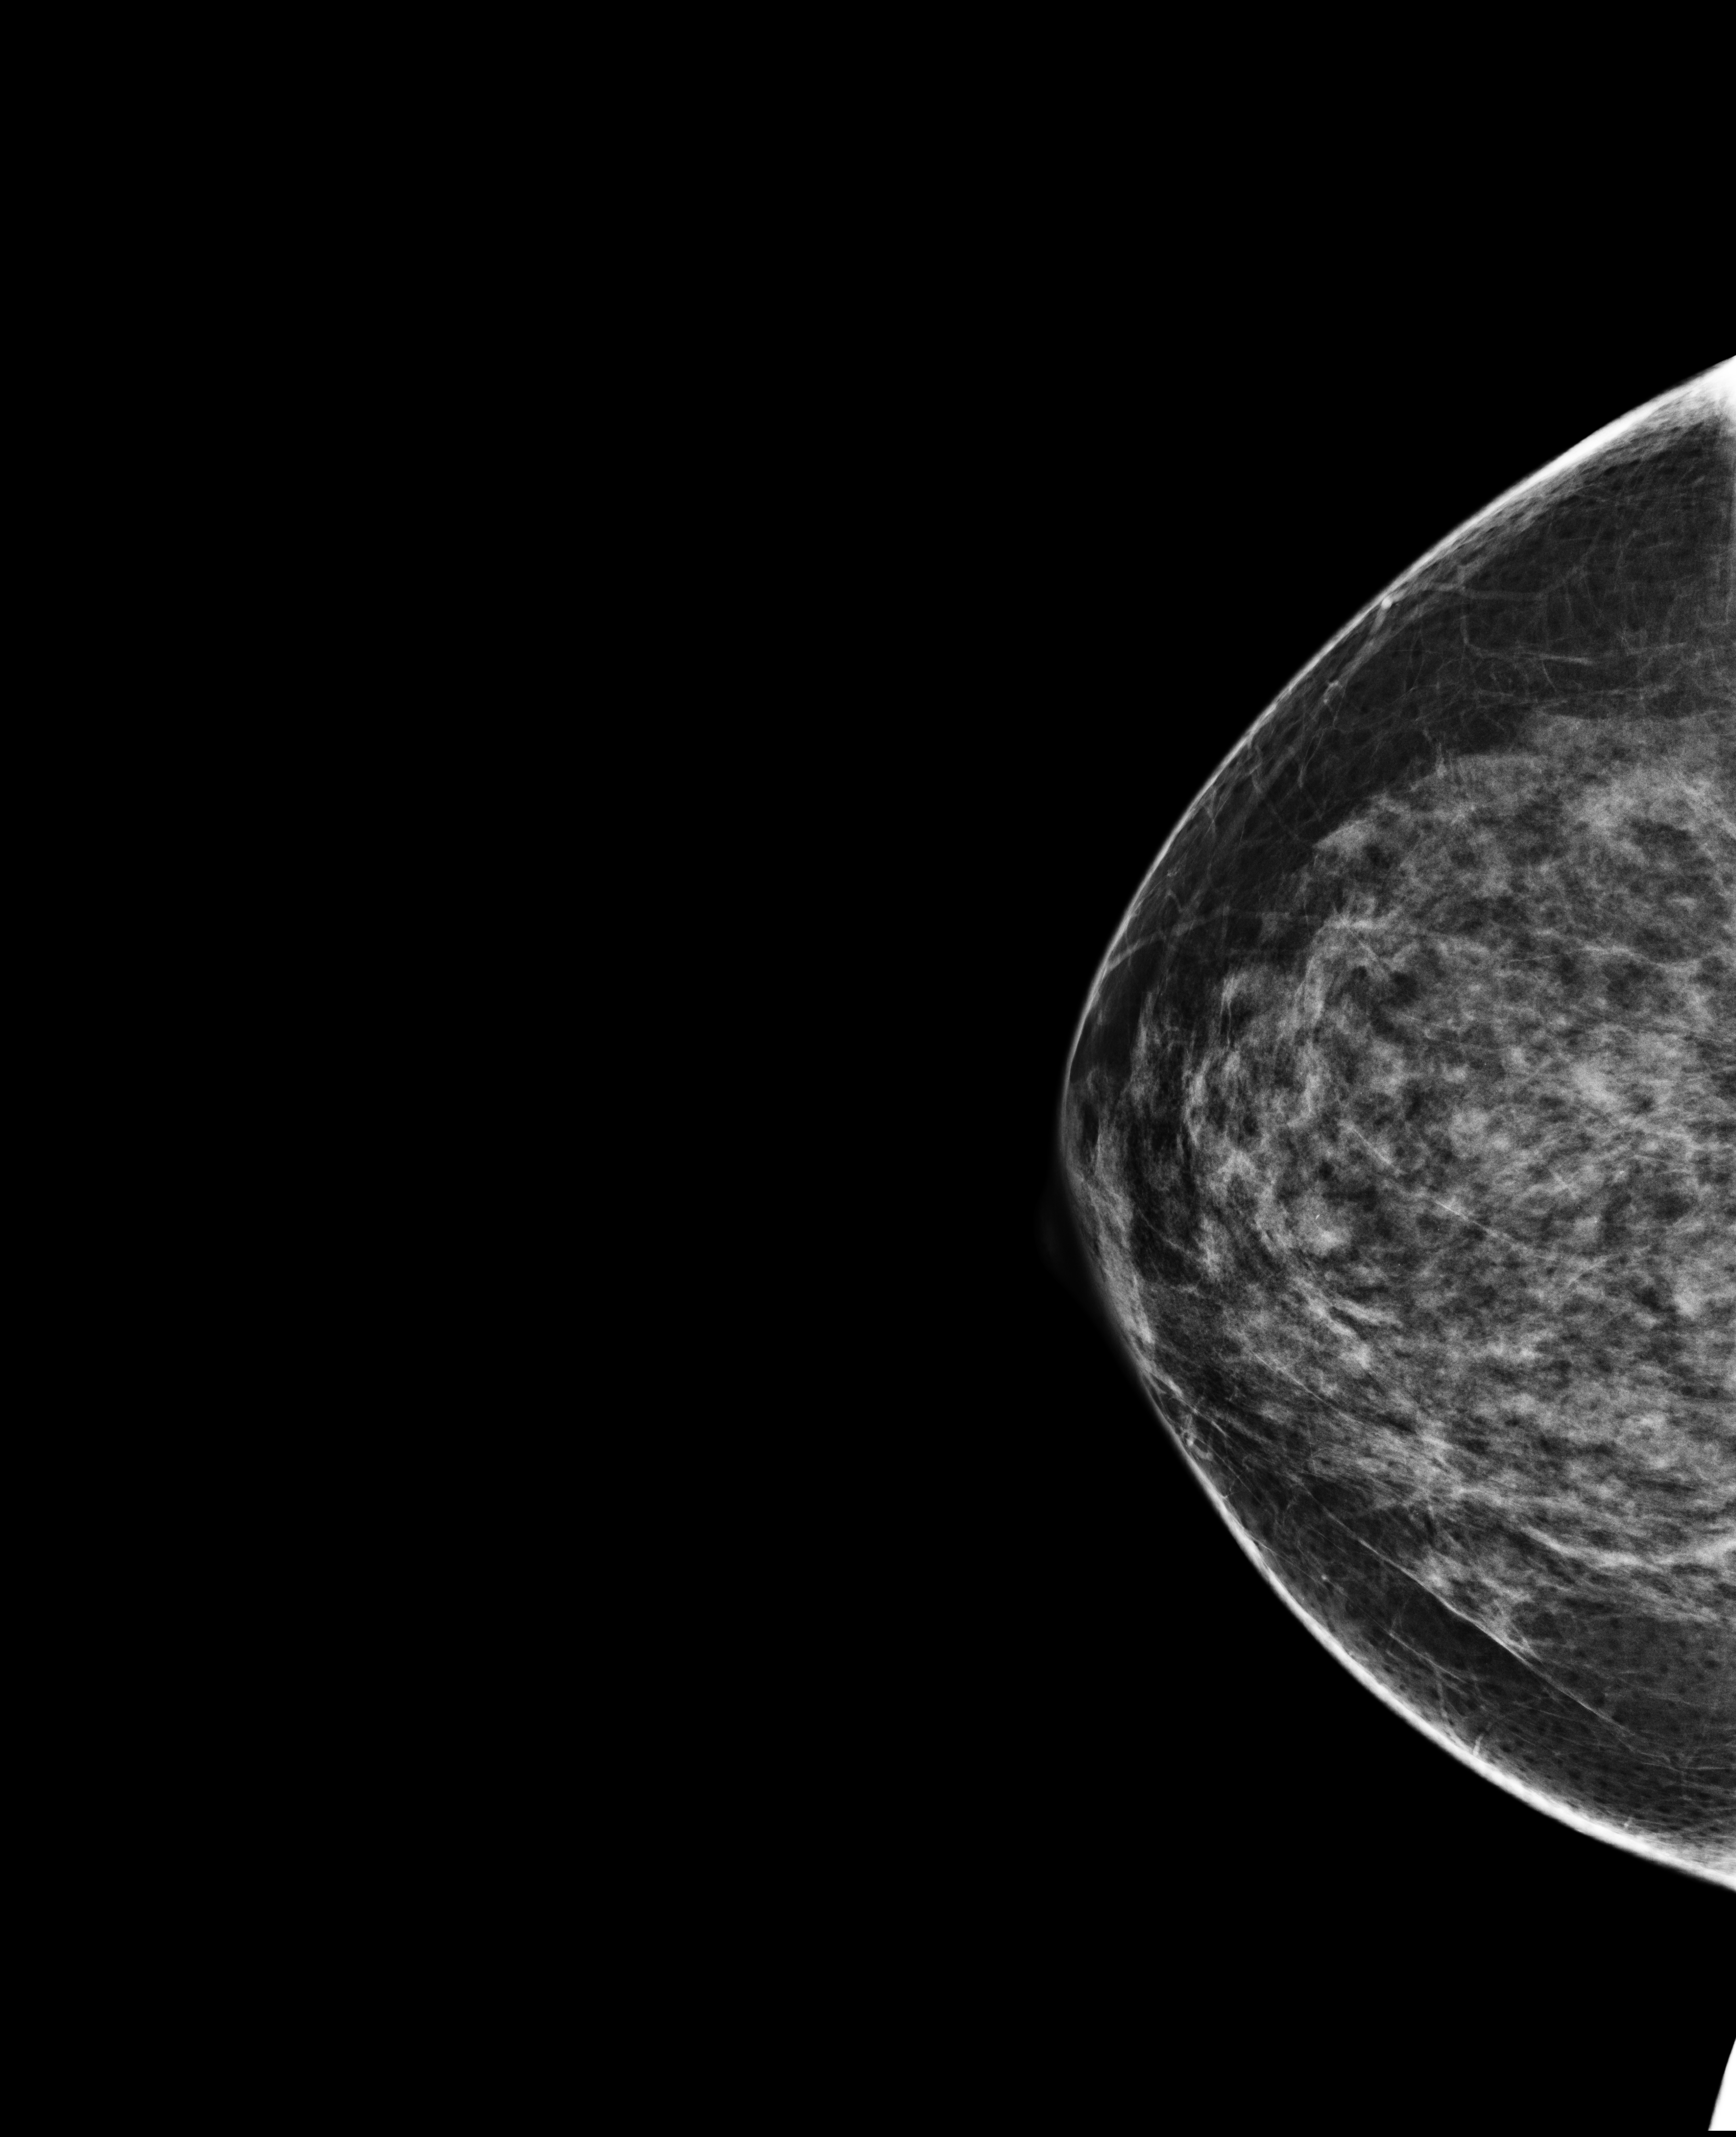
Annual screening mammography examination. Patient aged 53 years (female).
Image type: full-field digital mammogram. Breast: right. Projection: CC view.